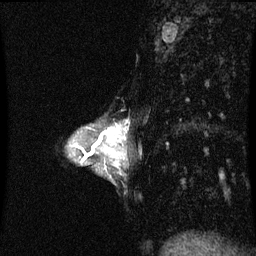
Breast MRI (dynamic contrast-enhanced), one sagittal slice. Position 23 of 60 along the scan axis. Dynamic contrast-enhanced series, image 2 of 3 at this slice position (ordered by acquisition). 1.5 T. TE 4.2 ms, TR 8.9 ms. 2 mm slice thickness. 256 × 256 image matrix, field of view 200 × 200 mm. Patient: female, 33 years. Case-level facts recorded for this patient, not image findings: setting: breast cancer imaged before/during neoadjuvant chemotherapy; receptor status: HER2-positive.
Outlined on this slice (semi-automatic segmentation, software-assisted and operator-edited):
- analysis volume of interest (the breast-tissue region the enhancement analysis was run in; not a lesion): box from (x=95, y=128) to (x=127, y=153) px
- tumour enhancement mask (voxels above the 70 % enhancement threshold inside the analysis volume of interest): (x=95, y=130)–(x=115, y=147)